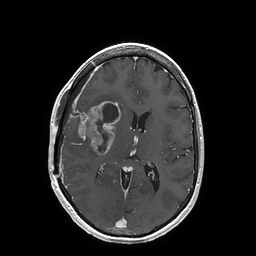
Brain MRI from a brain-tumour surgery series, one axial slice; slice 79 of 202 in the series (ordered by position); T1-weighted post-contrast; 1 mm slice thickness; 256 × 256 image matrix. From the clinical record (not read from this slice): histopathology: Glioblastoma; WHO grade: 4; IDH mutation: no; tumour location: Right Insular.
Structures marked on this image (manually delineated by an expert):
- tumour: bounding box <69,101,121,155> (left, top, right, bottom; pixels)